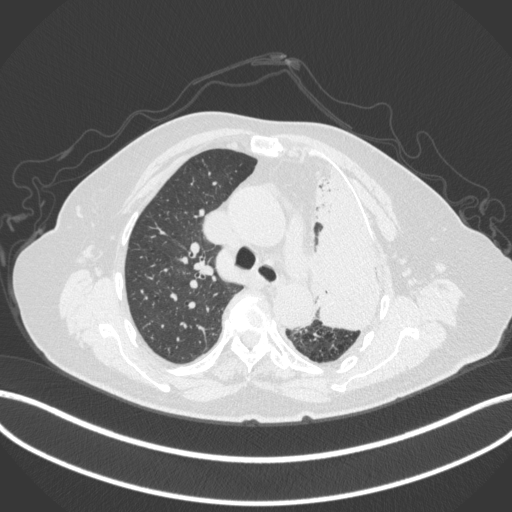
Chest CT, one axial slice. Position 275 of 399 along the scan axis. Reconstruction kernel B31f. Lung window (W 1500 / L -600 HU). 1 mm slice thickness. 512 × 512 image matrix. Female patient, age 75 years. From the clinical record (not read from this slice): clinical TNM (as recorded): T3 N3 M1.
Annotated regions visible in this slice (rectangle marked by the reading radiologist):
- lung tumour (recorded histology: adenocarcinoma): bounding box (x1, y1, x2, y2) in pixels: (312, 161, 386, 336)